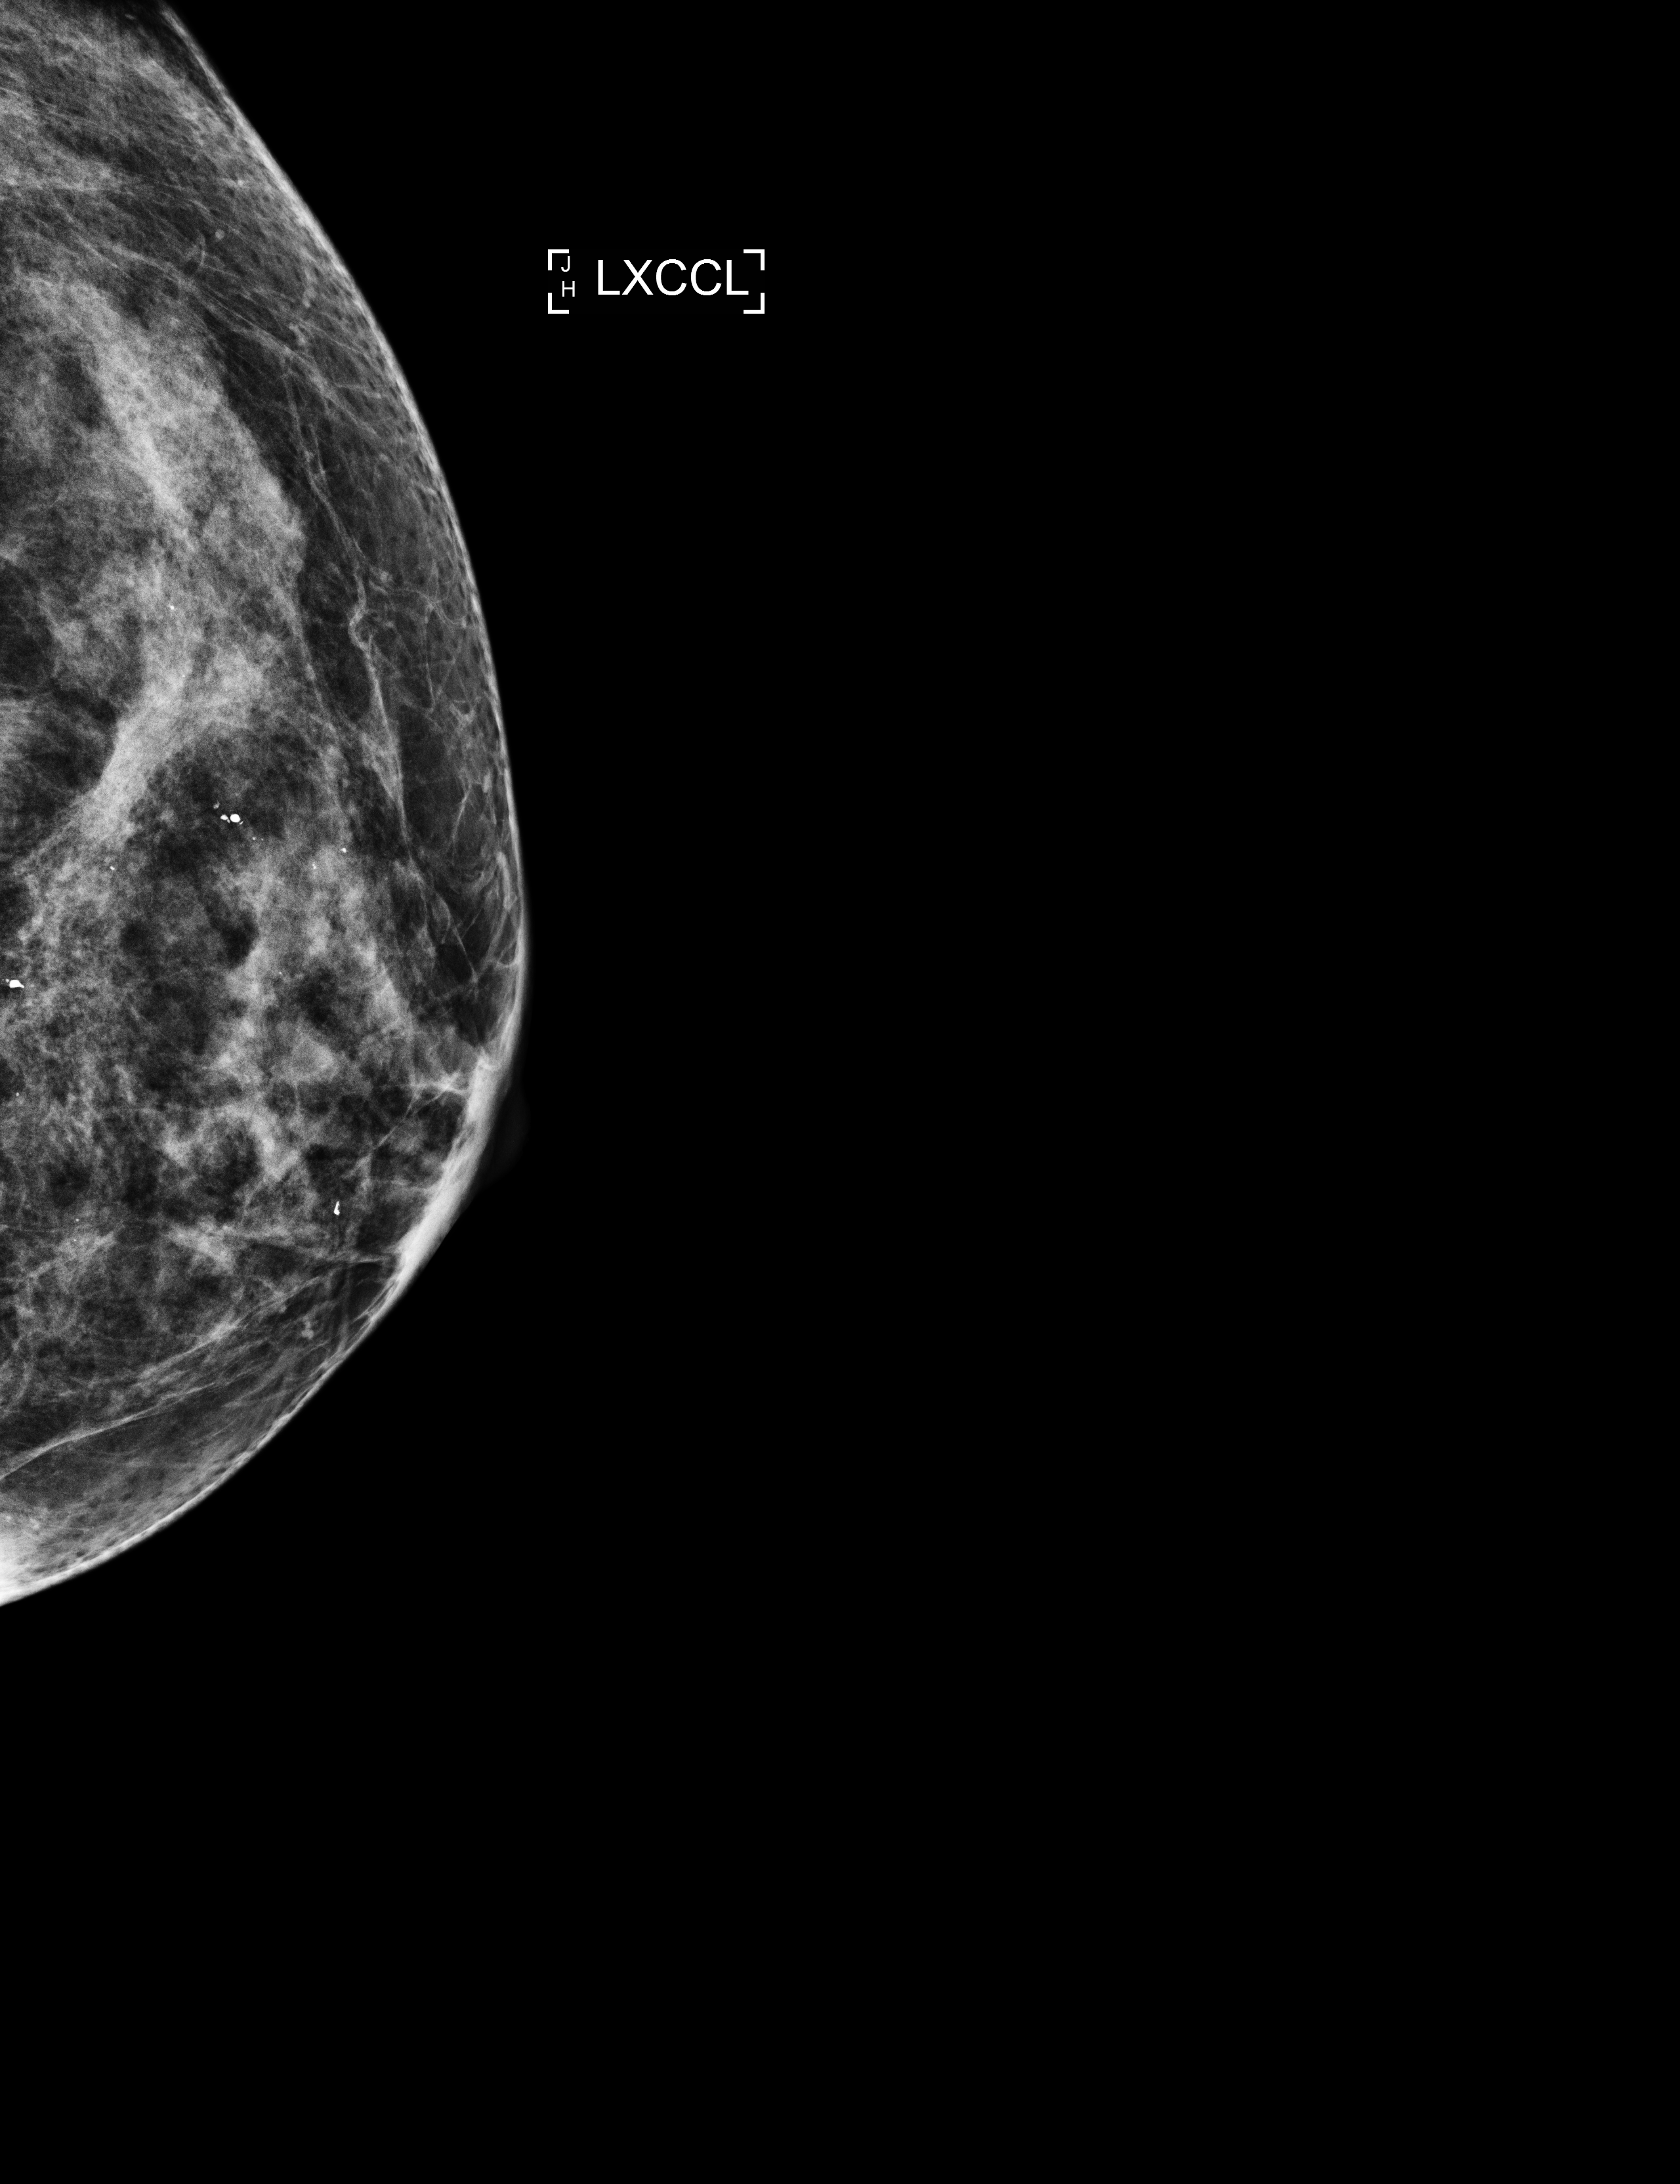
Digital mammogram (FFDM); left breast; exaggerated CC view (lateral); annual screening mammography examination; compressed breast thickness 44 mm. Patient aged 74 years (female).
- breast density at the screening exam (both breasts): heterogeneously dense (BI-RADS density category c)
- final BI-RADS assessment for this screening round (tomosynthesis exam, both breasts): category 2
- recall: no recall after this screen